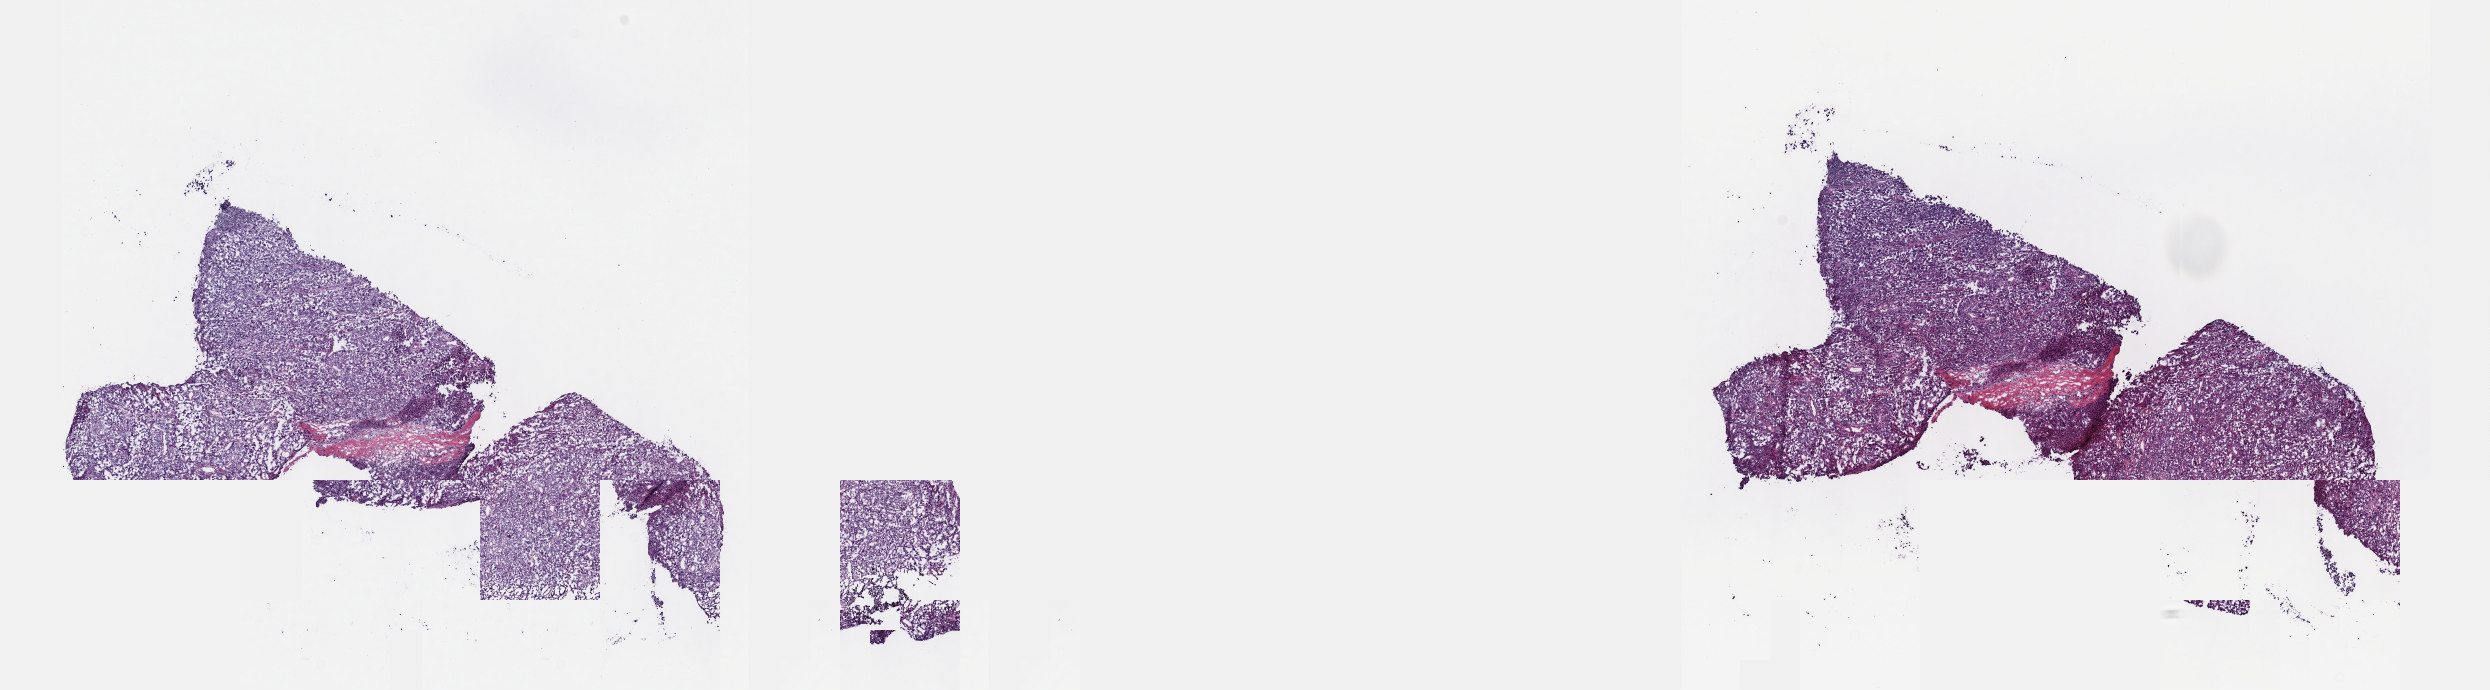
Whole-slide histology image, Hematoxylin and eosin (H&E) stained, whole scanned area (about 20.1 x 5.6 mm, acquisition: 40x scan) shown as a low-resolution overview; frozen section from the top of the tissue portion; metastatic tumour sample, sampled site: connective, subcutaneous and other soft tissues of thorax. Patient: male, age at initial diagnosis 62 years. Slide review estimates, as recorded: tumour cells 100%, tumour nuclei 80%, normal cells 0%, stromal cells 0%, necrosis 0%. Inflammatory infiltration, as recorded: lymphocyte infiltration 3%, monocyte infiltration 0%, neutrophil infiltration 0%.
This section: metastatic tumour tissue. Patient diagnosis: Malignant melanoma, NOS.